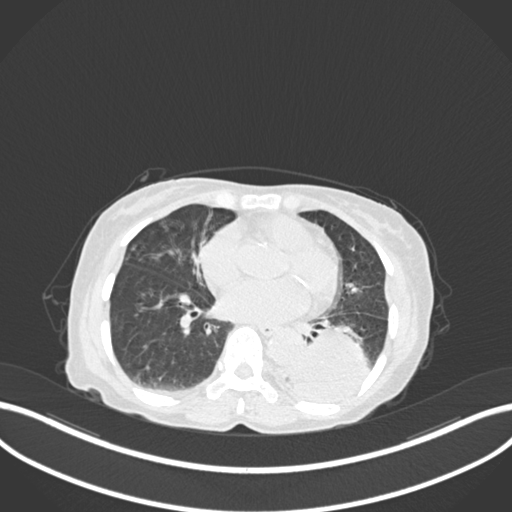
Chest CT, one axial slice. 120 kVp. Lung window (W 1500 / L -600 HU). 512 × 512 image matrix, field of view 400 × 400 mm. Female patient, age 78 years. Case-level facts recorded for this patient, not image findings: clinical TNM (as recorded): T3 N0 M1.
Annotated regions visible in this slice (bounding box drawn by a radiologist):
- lung tumour (recorded histology: squamous cell carcinoma): box from (x=288, y=321) to (x=373, y=404) px